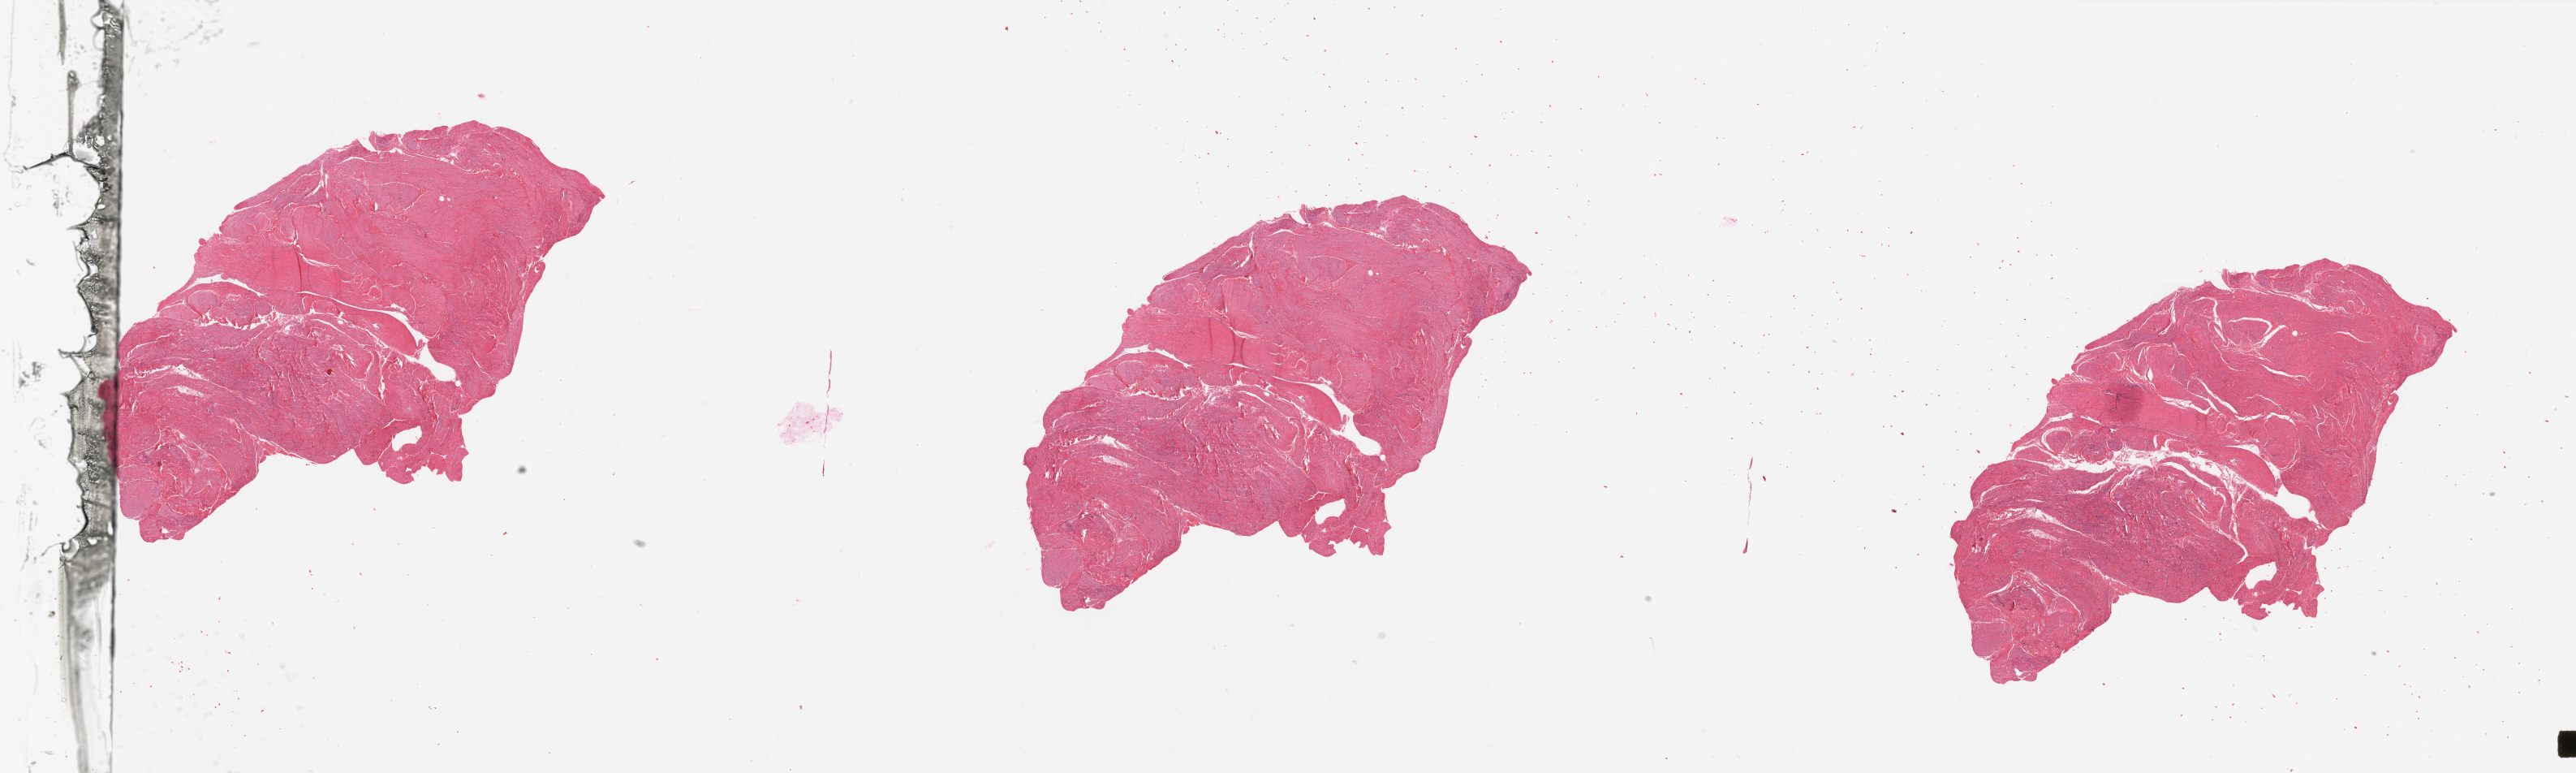
Digitized Hematoxylin and eosin (H&E) stained tissue section (whole slide), whole scanned area (about 50.2 x 15.1 mm) shown as a low-resolution overview, normal (non-tumour) tissue sample, uterus. 53-year-old female patient.
* this section: normal (non-tumour) tissue from the same patient
* patient diagnosis: Endometrioid adenocarcinoma, NOS